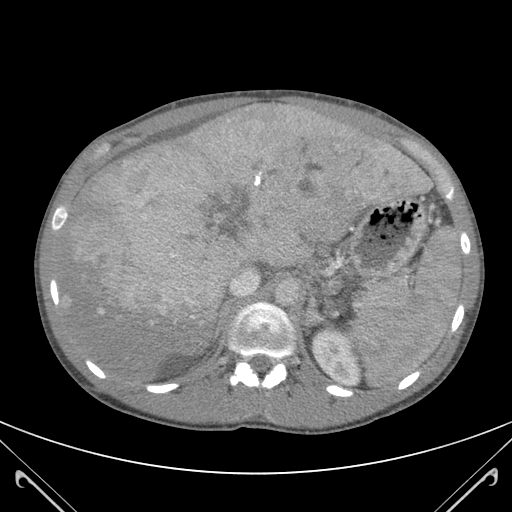
Contrast-enhanced abdominal CT (liver protocol), one axial slice. Slice 79 of 118 in the series (ordered by position). Soft-tissue window (W 400 / L 40 HU). 512 × 512 image matrix. From the clinical record (not read from this slice): diagnosis: hepatocellular carcinoma (patient treated with transarterial chemoembolisation; whether this scan precedes or follows treatment is not stated here); TNM stage (as recorded): Stage-IIIB; Child-Pugh class: A.
Outlined on this slice (semi-automatically segmented with operator editing):
- abdominal aorta: box from (x=274, y=282) to (x=298, y=307) px
- liver parenchyma outside the tumour (the mass and vessels are separate outlines, so this box may not span the whole liver): (x=59, y=107)–(x=423, y=378)
- mass: (x=80, y=111)–(x=422, y=342)
- liver vessels: (x=79, y=110)–(x=422, y=314)